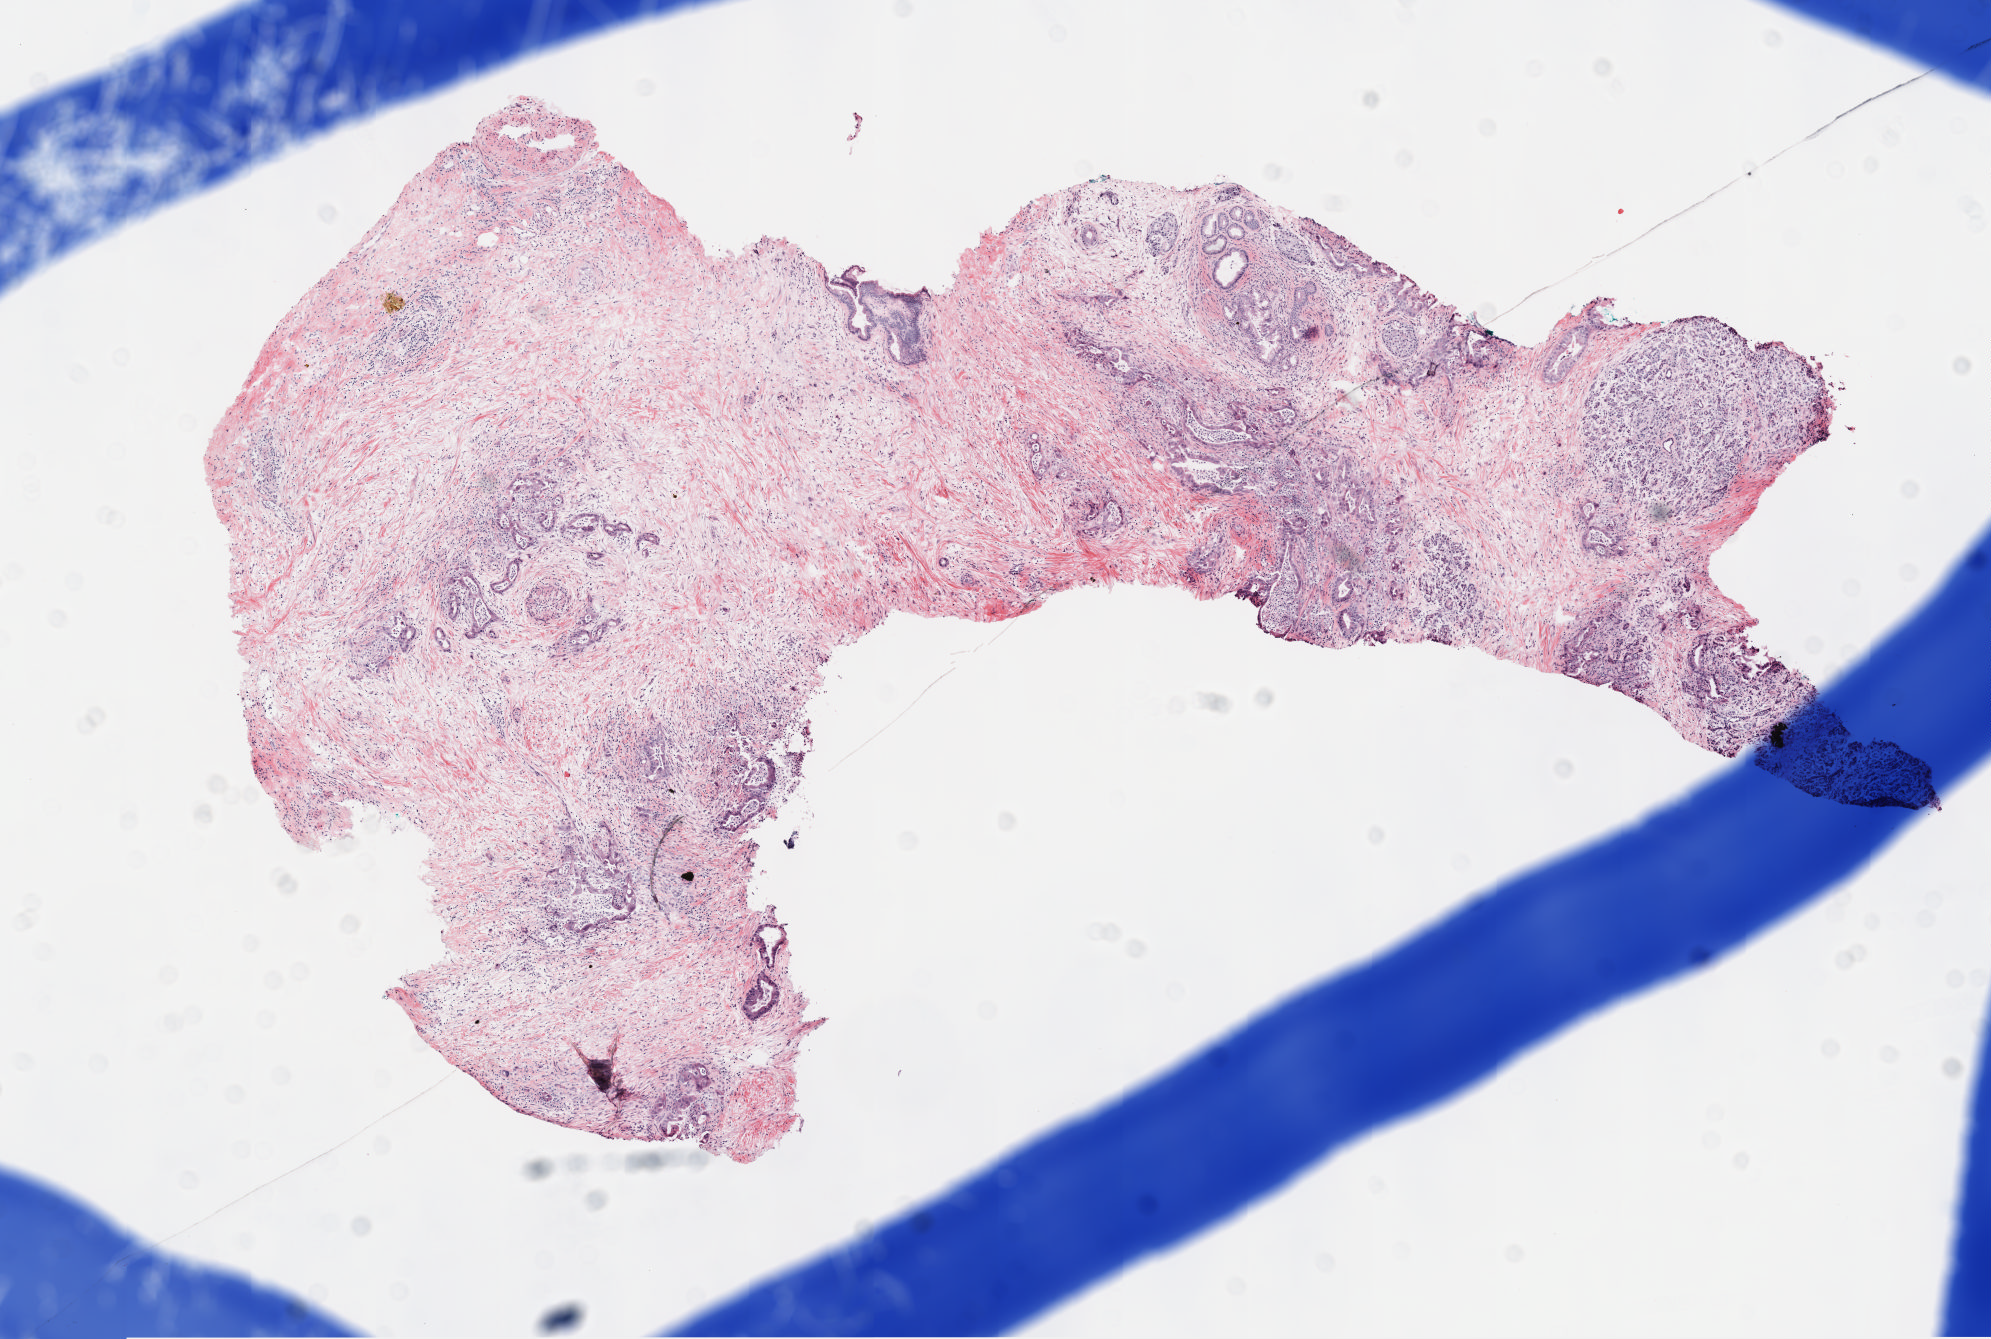
Digitized H&E tissue section (whole slide), whole scanned area (about 8.1 x 5.4 mm) shown as a low-resolution overview; frozen section; pancreas, primary tumour sample. Male, age 67 years at initial diagnosis. Histologic grade: G3 (poorly differentiated). Slide review estimates, as recorded: tumour cells 50%, tumour nuclei 10%, normal cells 20%, stromal cells 30%, necrosis 0%. Inflammatory infiltration, as recorded: lymphocyte infiltration 0%, monocyte infiltration 0%, neutrophil infiltration 0%.
* AJCC pathologic stage: IIB
* diagnosis: Infiltrating duct carcinoma, NOS (body of pancreas)
* TNM: T3 N1 MX
* lymph nodes positive (case pathology): 5 of 23 examined